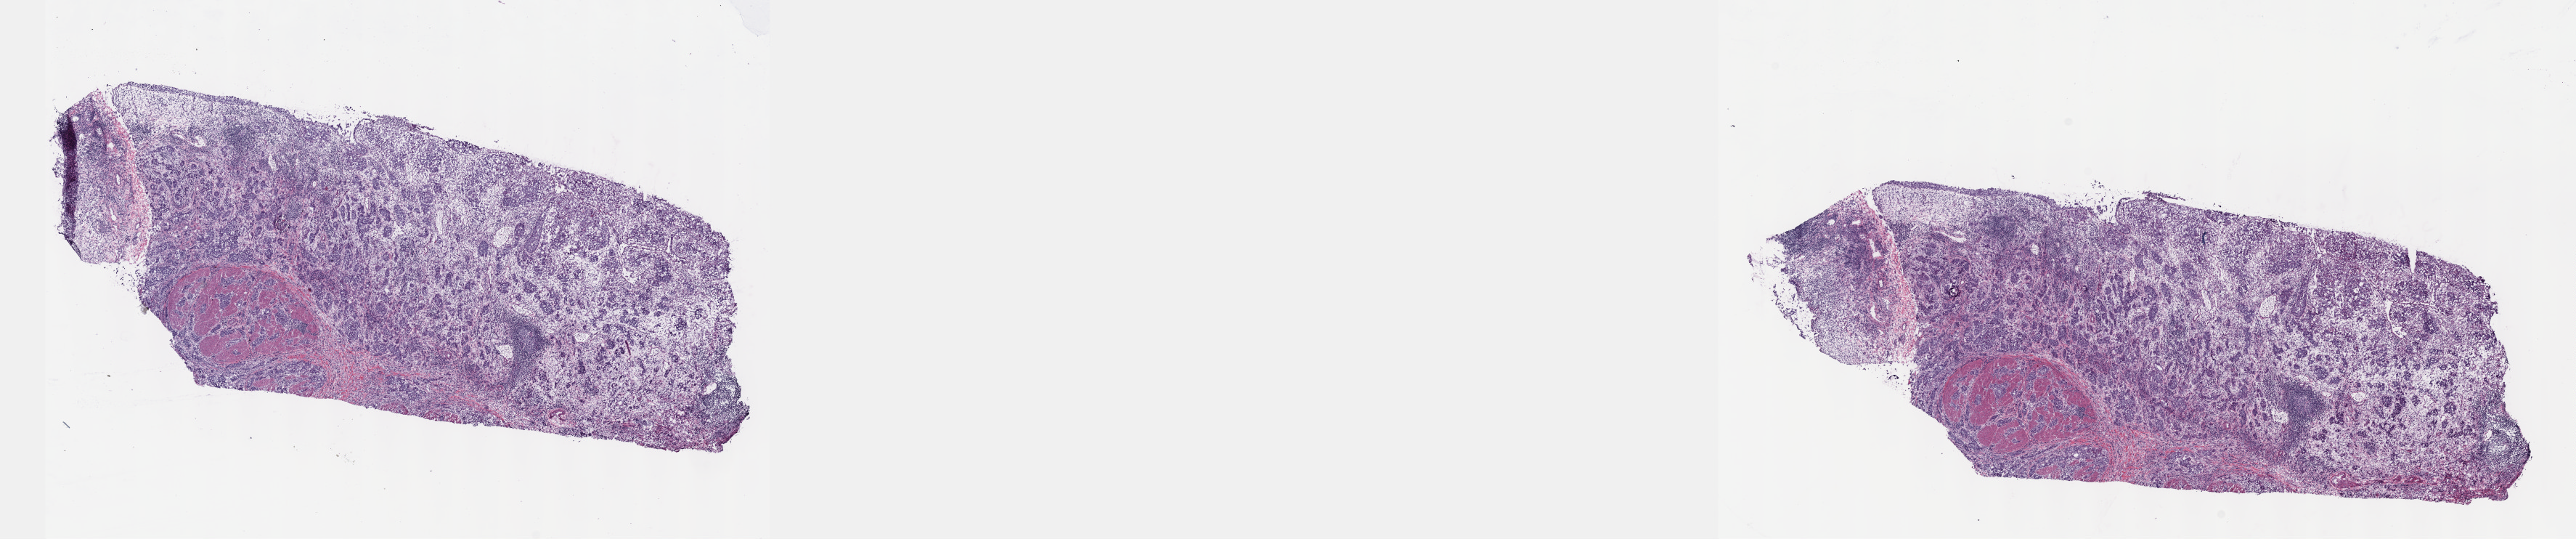
Digitized Hematoxylin and eosin (H&E) stained tissue section (whole slide) — low-resolution overview of the scanned area, about 28.7 x 6.0 mm (acquisition: 40x scan); frozen section; primary tumour sample from the bladder. Male, age 77 years at initial diagnosis. Pathologist review of this section (percent, as recorded): tumour cells 50%, tumour nuclei 60%, normal cells 10%, stromal cells 40%, necrosis 0%. Infiltration values recorded for this section: lymphocyte infiltration 0%, monocyte infiltration 0%, neutrophil infiltration 0%.
- AJCC pathologic stage: IV (7th edition)
- diagnosis: Transitional cell carcinoma